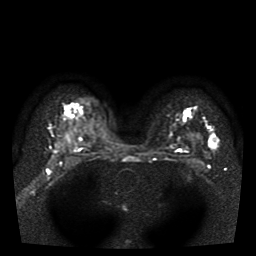
Breast MRI, one axial slice. Position 29 of 41 along the scan axis. Diffusion-weighted series; image 2 of 3 stored at this slice position (different b-values; order by instance number). 1.5 T. 5 mm slice thickness. 256 × 256 image matrix, field of view 330 × 330 mm. Female patient.
Outlined on this slice (expert manual segmentation):
- tumour on diffusion-weighted imaging: bounding box (x1, y1, x2, y2) in pixels: (209, 135, 219, 149)